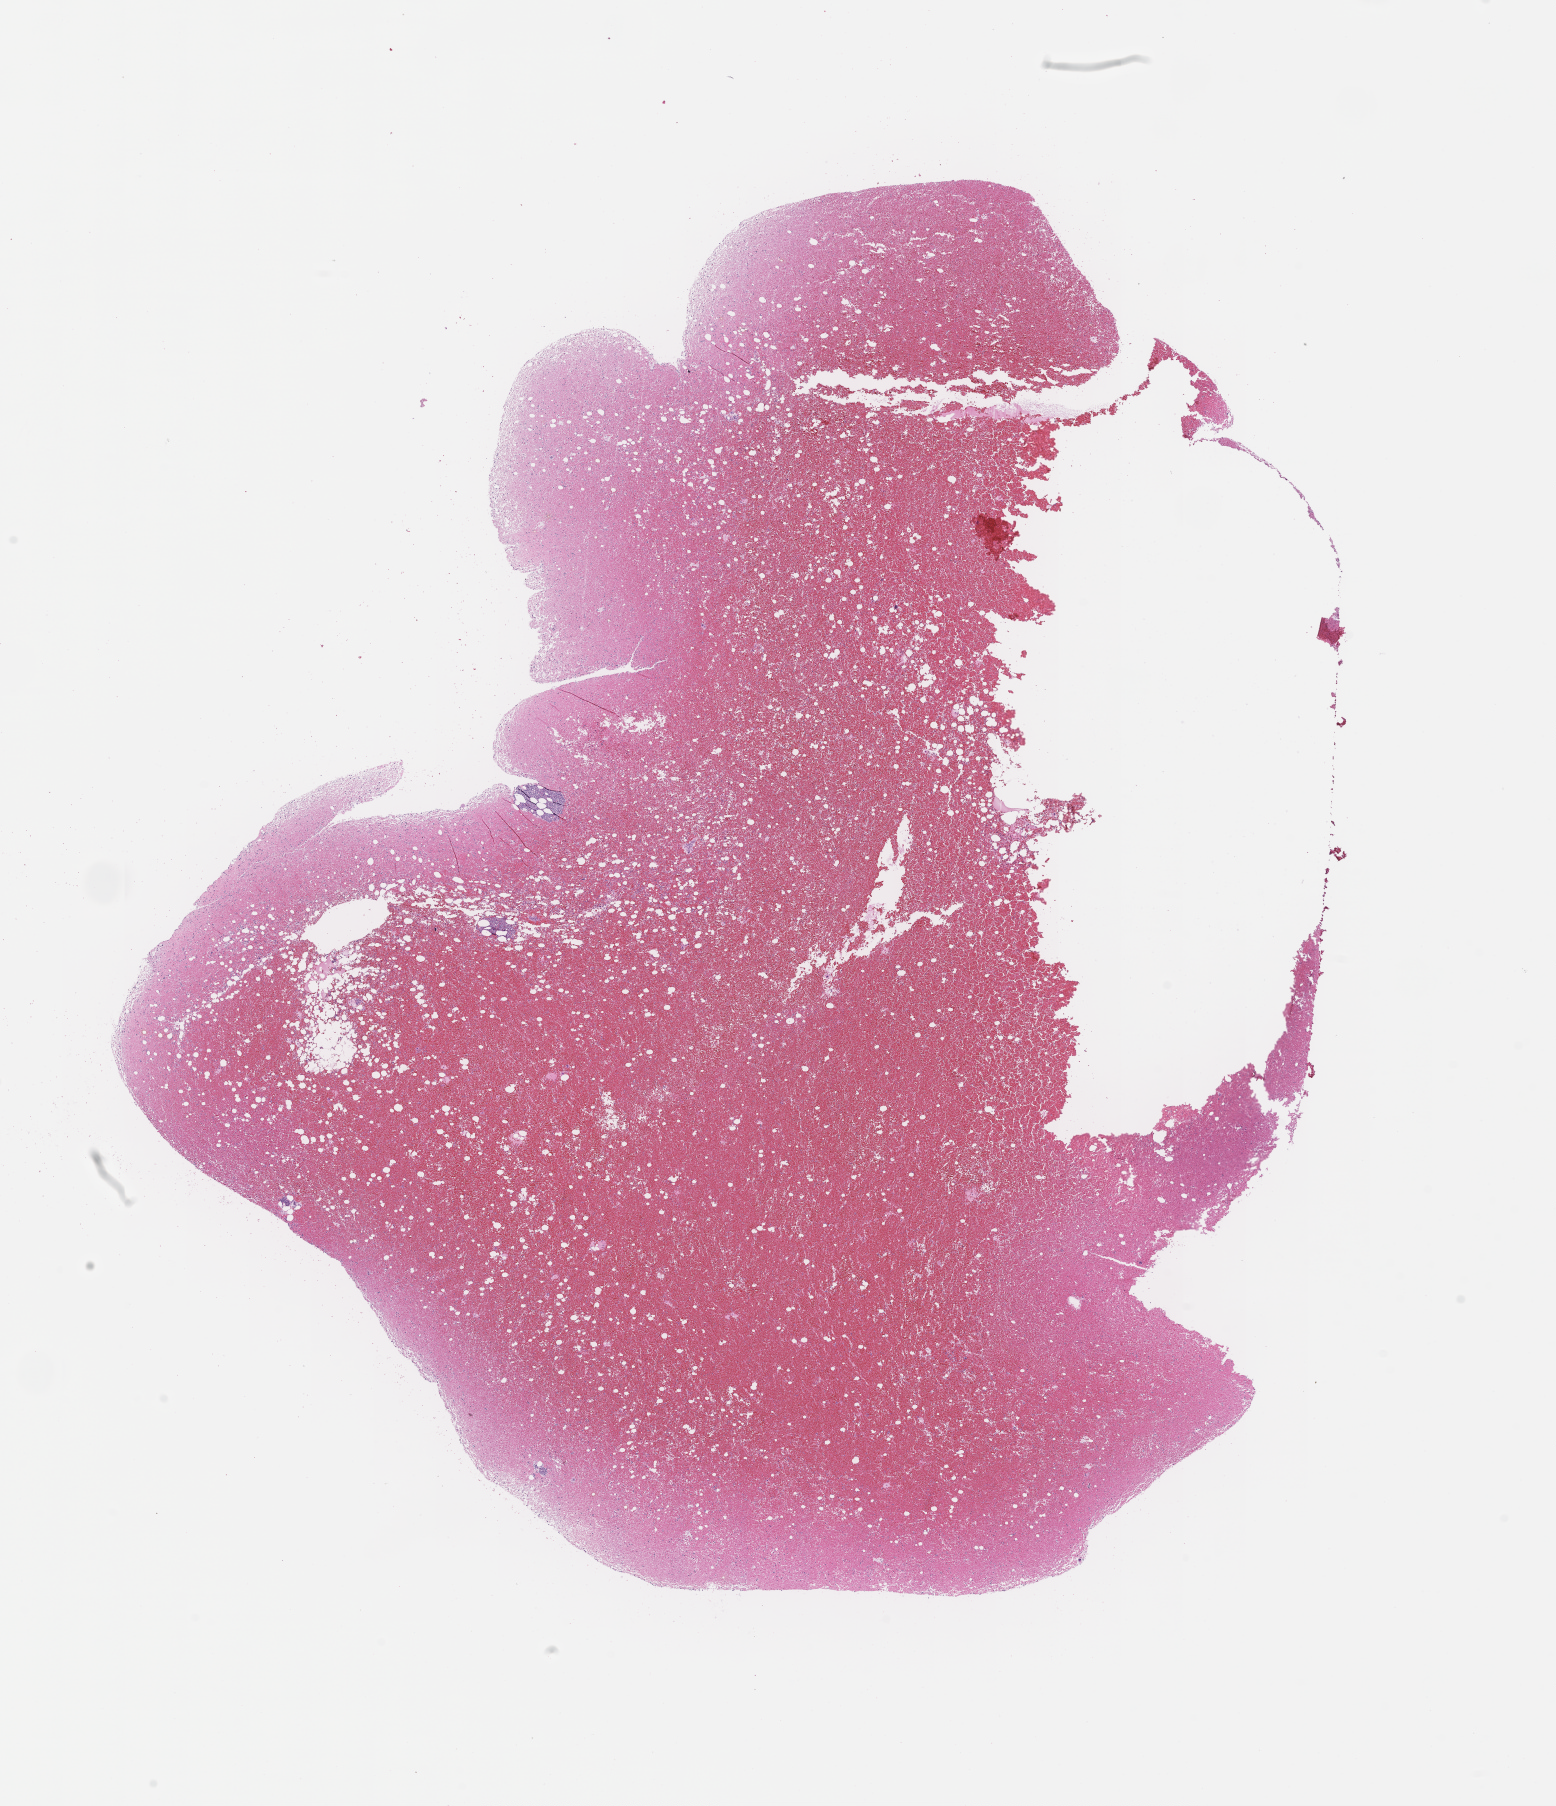
Digitized hematoxylin and eosin (H&E)-stained section, shown as a low-resolution overview of the whole scanned area (about 12.6 x 14.6 mm). FFPE section. Site: bone marrow. Archival tissue. Patient sex: female.
• this section: primary tumor
• diagnosis: Plasma Cell Myeloma